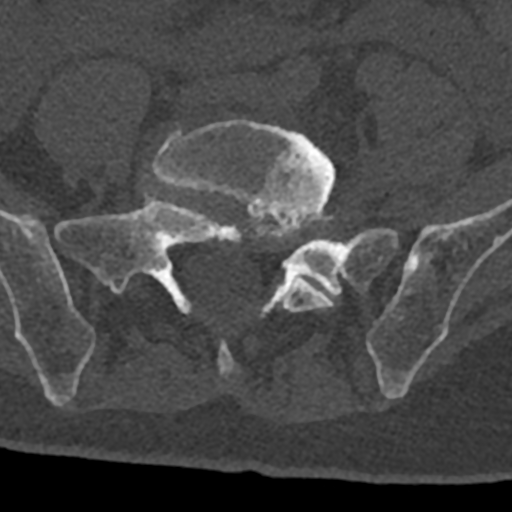
CT including the spine, one axial slice. Position 173 of 797 along the scan axis. Reconstruction kernel Br40s/3. Bone window (W 1800 / L 400 HU). 512 × 512 image matrix, field of view 160 × 160 mm. Male patient, age 74 years. Case-level facts recorded for this patient, not image findings: primary cancer: renal; vertebrae with lytic lesions (as recorded): T10, L1, L2, L3, L4, L5.
Annotated regions visible in this slice (semi-automatically segmented with operator editing):
- L5 vertebra: bounding box (x1, y1, x2, y2) in pixels: (152, 119, 336, 374)